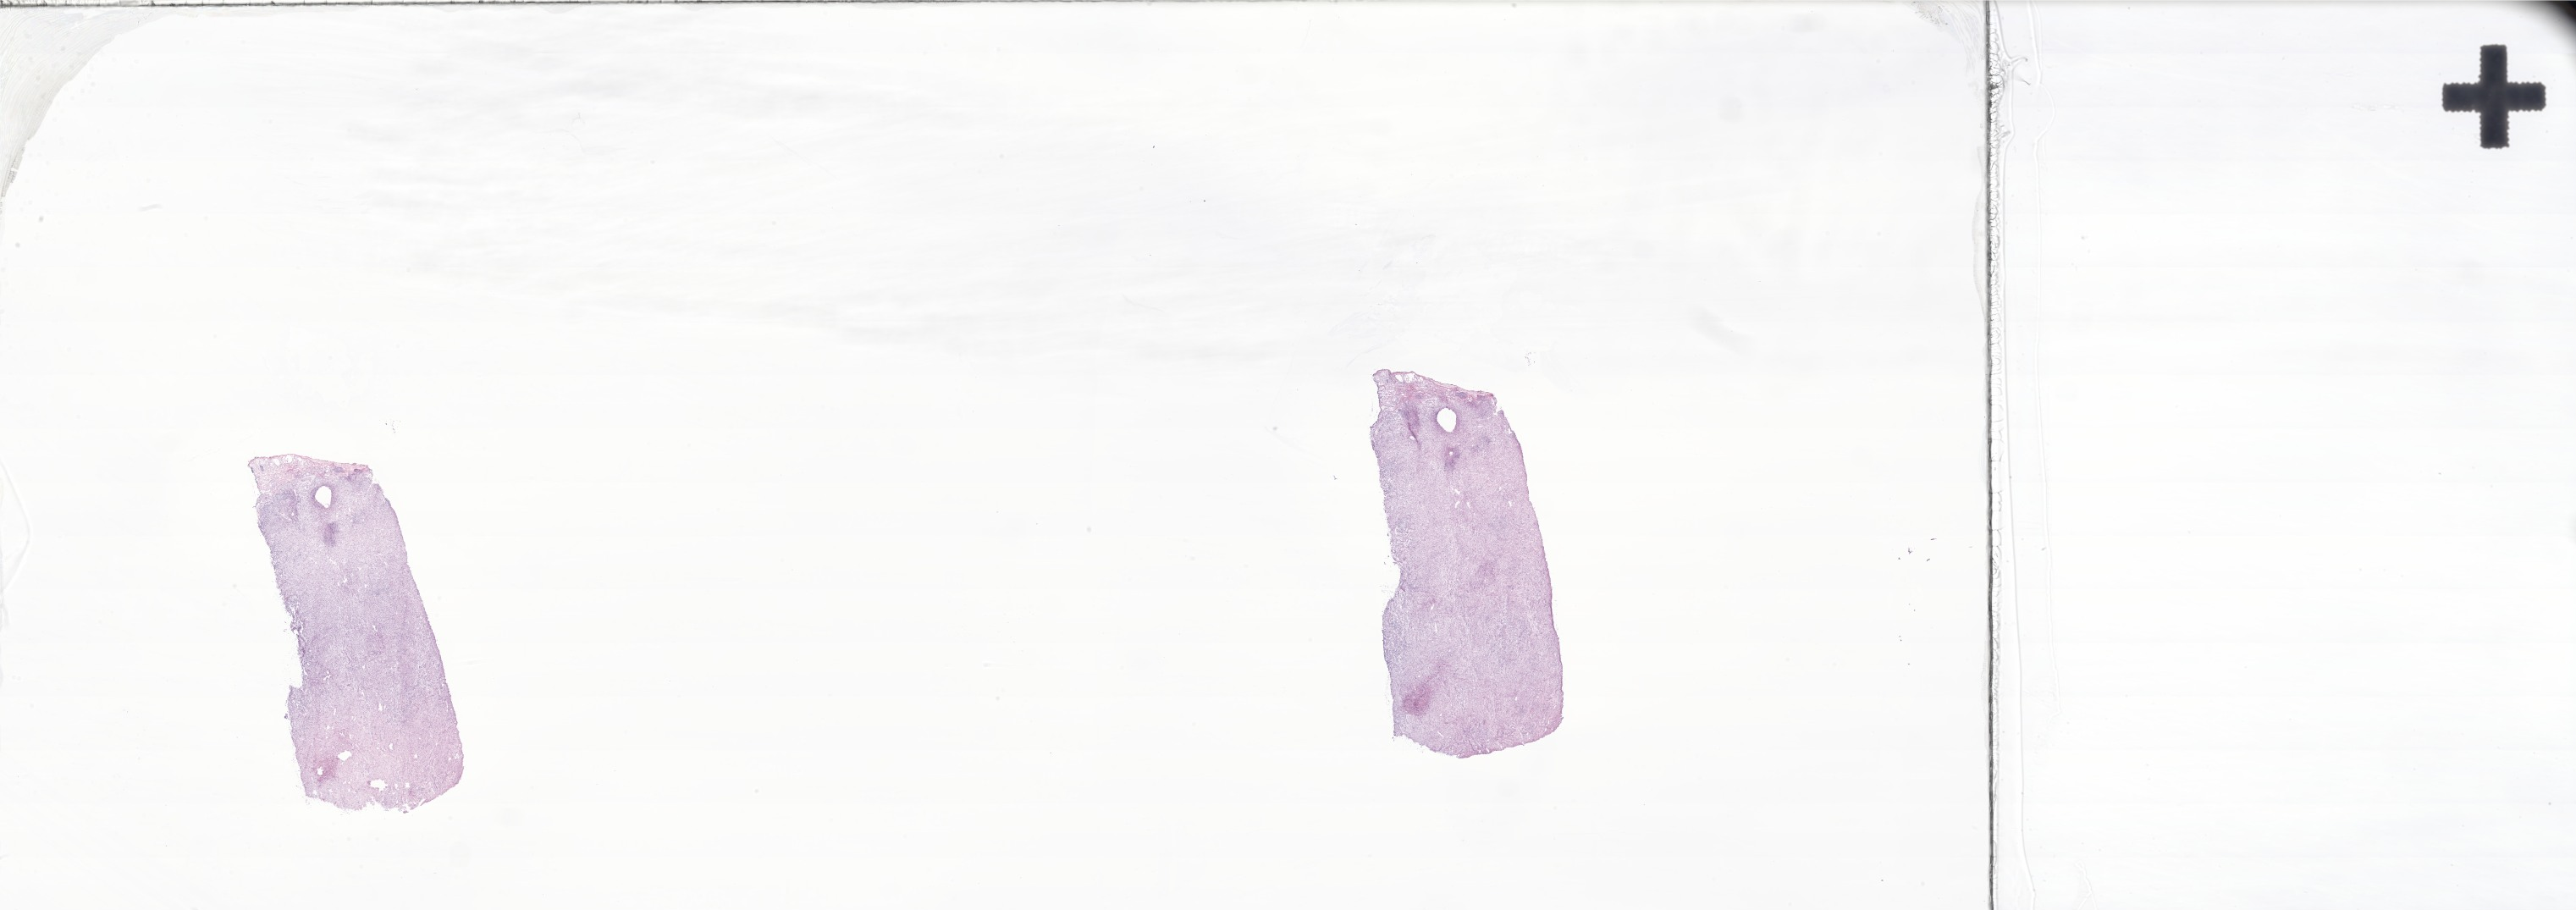
H&E whole-slide image of tumor tissue from the abdomen — shown as a low-resolution overview of the whole scanned area (about 51.3 x 18.1 mm), cryosection (OCT / tissue freezing medium). Patient: female, age 78 months.
* diagnosis: Myofibroblastic tumor, NOS